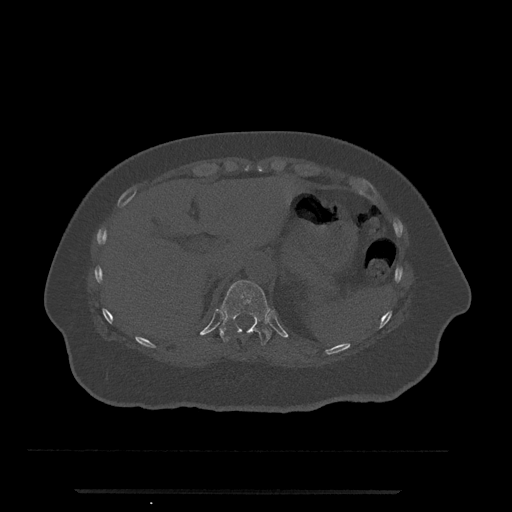
CT including the spine, one axial slice. Position 240 of 797 along the scan axis. 120 kVp. Bone window (W 1800 / L 400 HU). 0.5 mm slice thickness. 512 × 512 image matrix, field of view 440 × 440 mm. Patient: female, 51 years. Case-level facts recorded for this patient, not image findings: primary cancer: neuro; vertebrae with lytic lesions (as recorded): T8.
Outlined on this slice (semi-automatic segmentation, software-assisted and operator-edited):
- T11 vertebra: bounding box (x1, y1, x2, y2) in pixels: (219, 280, 271, 346)